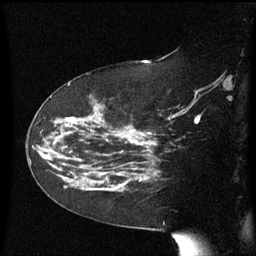
Breast MRI (dynamic contrast-enhanced), one sagittal slice. Position 36 of 60 along the scan axis. Dynamic contrast-enhanced series, image 2 of 3 at this slice position (ordered by acquisition). 1.5 T. TE 4.2 ms, TR 8.4 ms. 2.3 mm slice thickness. 256 × 256 image matrix. Female patient, age 63 years. From the clinical record (not read from this slice): setting: breast cancer imaged before/during neoadjuvant chemotherapy; receptor status: HER2-positive.
Annotated regions visible in this slice (semi-automatically segmented with operator editing):
- analysis volume of interest (the breast-tissue region the enhancement analysis was run in; not a lesion): box from (x=63, y=144) to (x=147, y=192) px
- tumour enhancement mask (voxels above the 70 % enhancement threshold inside the analysis volume of interest): (x=97, y=144)–(x=147, y=191)